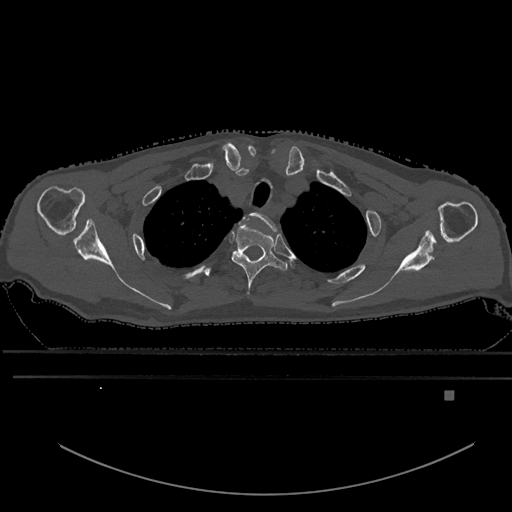
CT including the spine, one axial slice; slice 495 of 969 in the series (ordered by position); bone window (W 1800 / L 400 HU); 512 × 512 image matrix, field of view 456 × 456 mm. Male patient, age 82 years. From the clinical record (not read from this slice): primary cancer: prostate; vertebrae with lytic lesions (as recorded): T11, T9, T8, T2.
Outlined on this slice (semi-automatic segmentation, software-assisted and operator-edited):
- T1 vertebra: bounding box (x1, y1, x2, y2) in pixels: (251, 212, 277, 231)
- T2 vertebra: (231, 222, 288, 295)